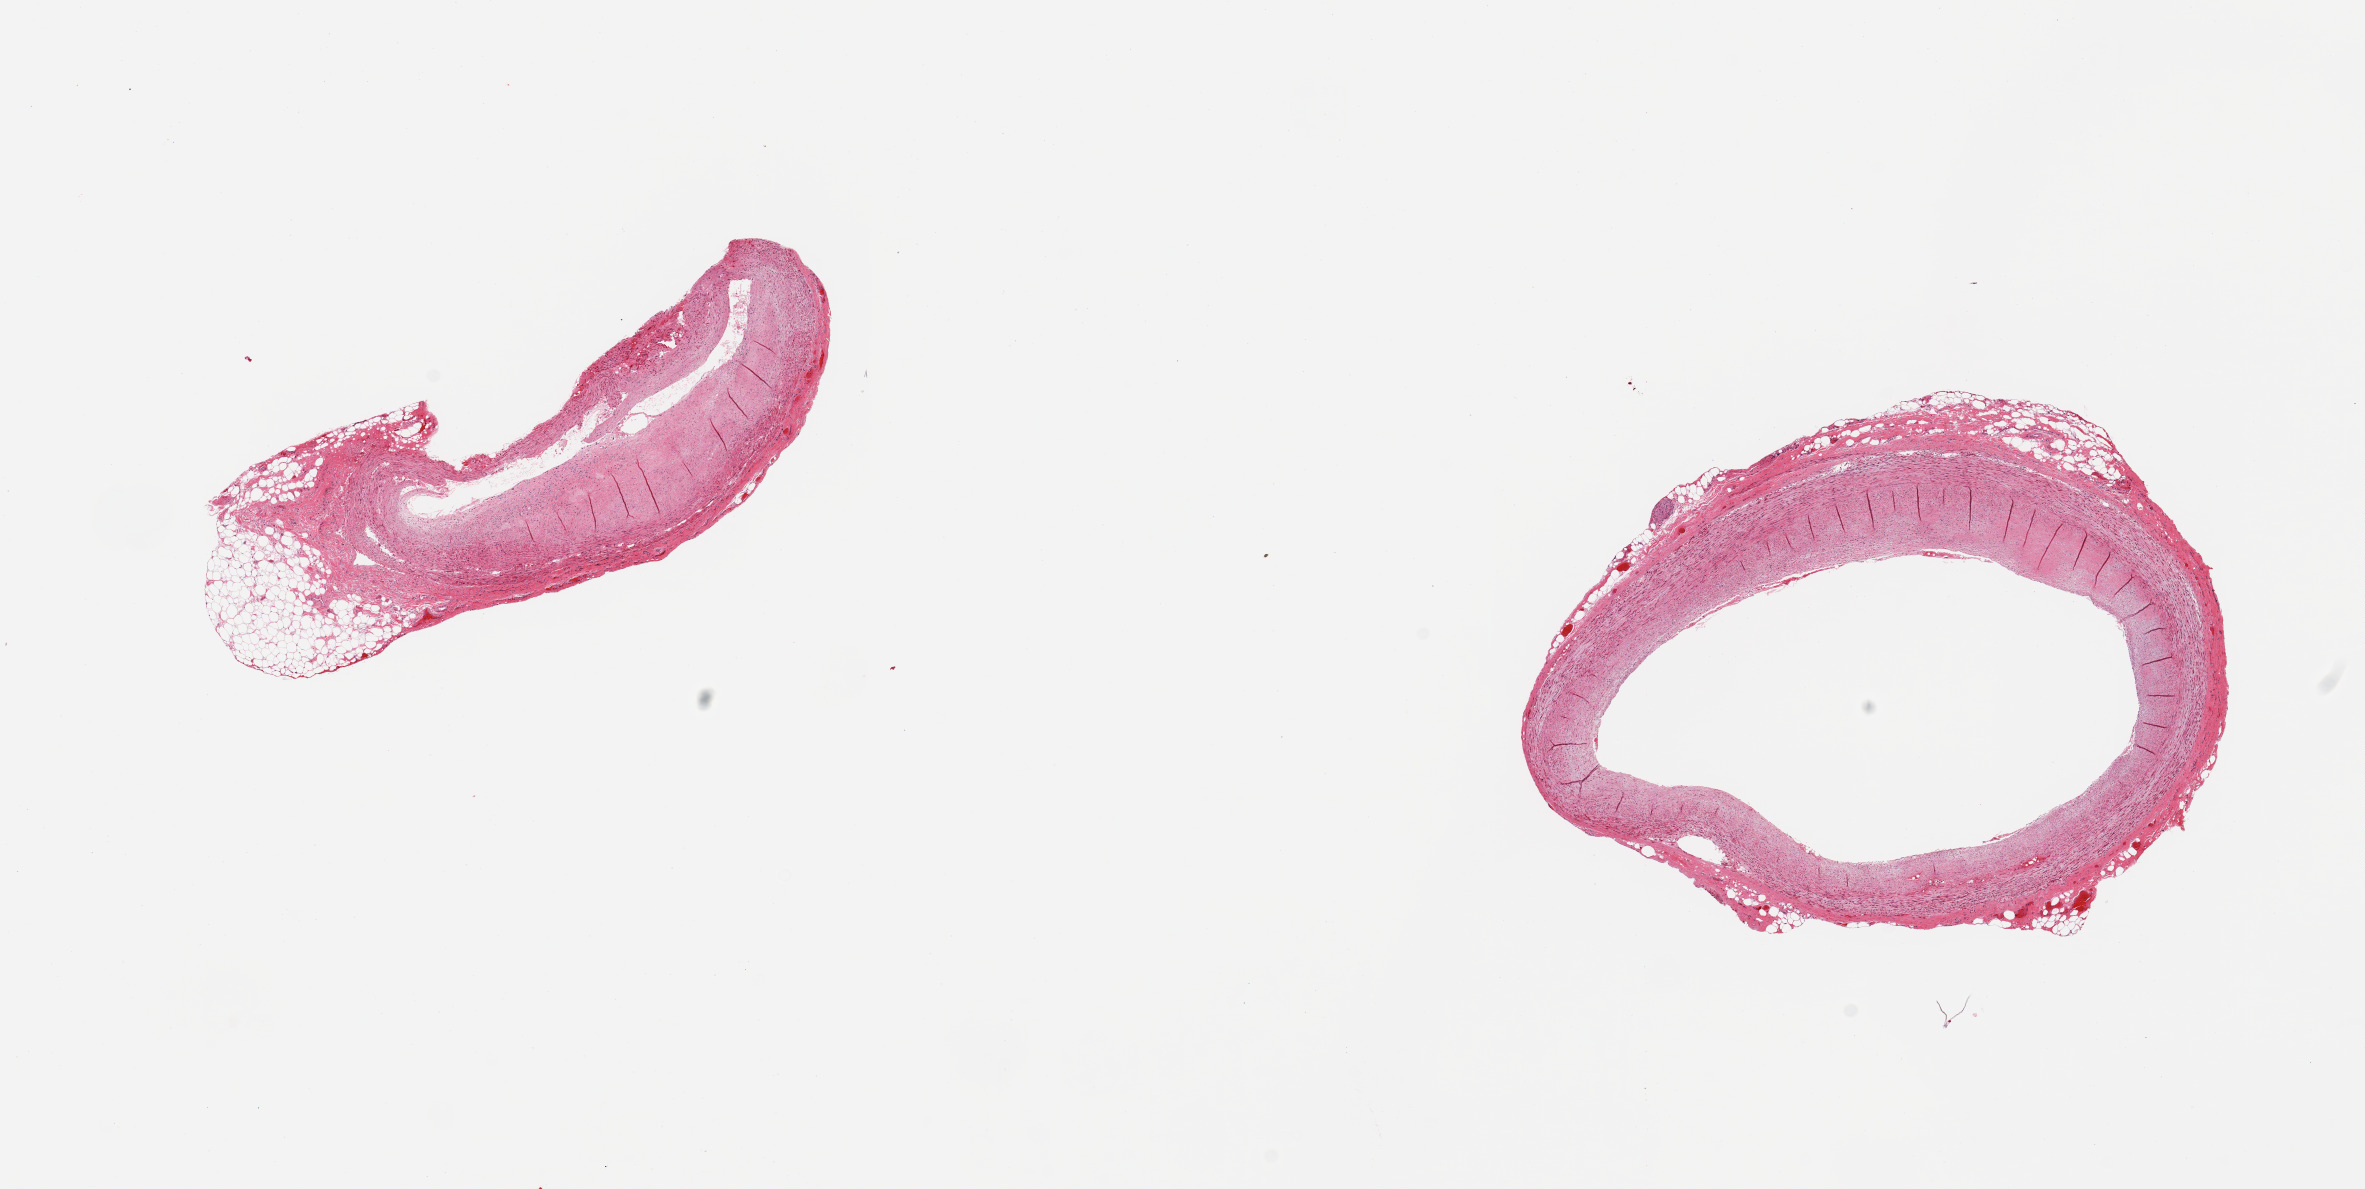
Hematoxylin and eosin (H&E) whole-slide image — a low-resolution overview of the entire scanned area, about 18.7 x 9.4 mm; PAXgene-fixed, paraffin-embedded tissue; sampled site (target tissue): coronary artery; tissue donor sample. Donor sex: male.
Reviewer comment on this tissue sample: 2 pieces; one with eccentric atheromatous plaque narrowing lumen and up to 1.025mm external fat; other with minimal amount of fat attached and atheromatous change with ~25% luminal narrowing.